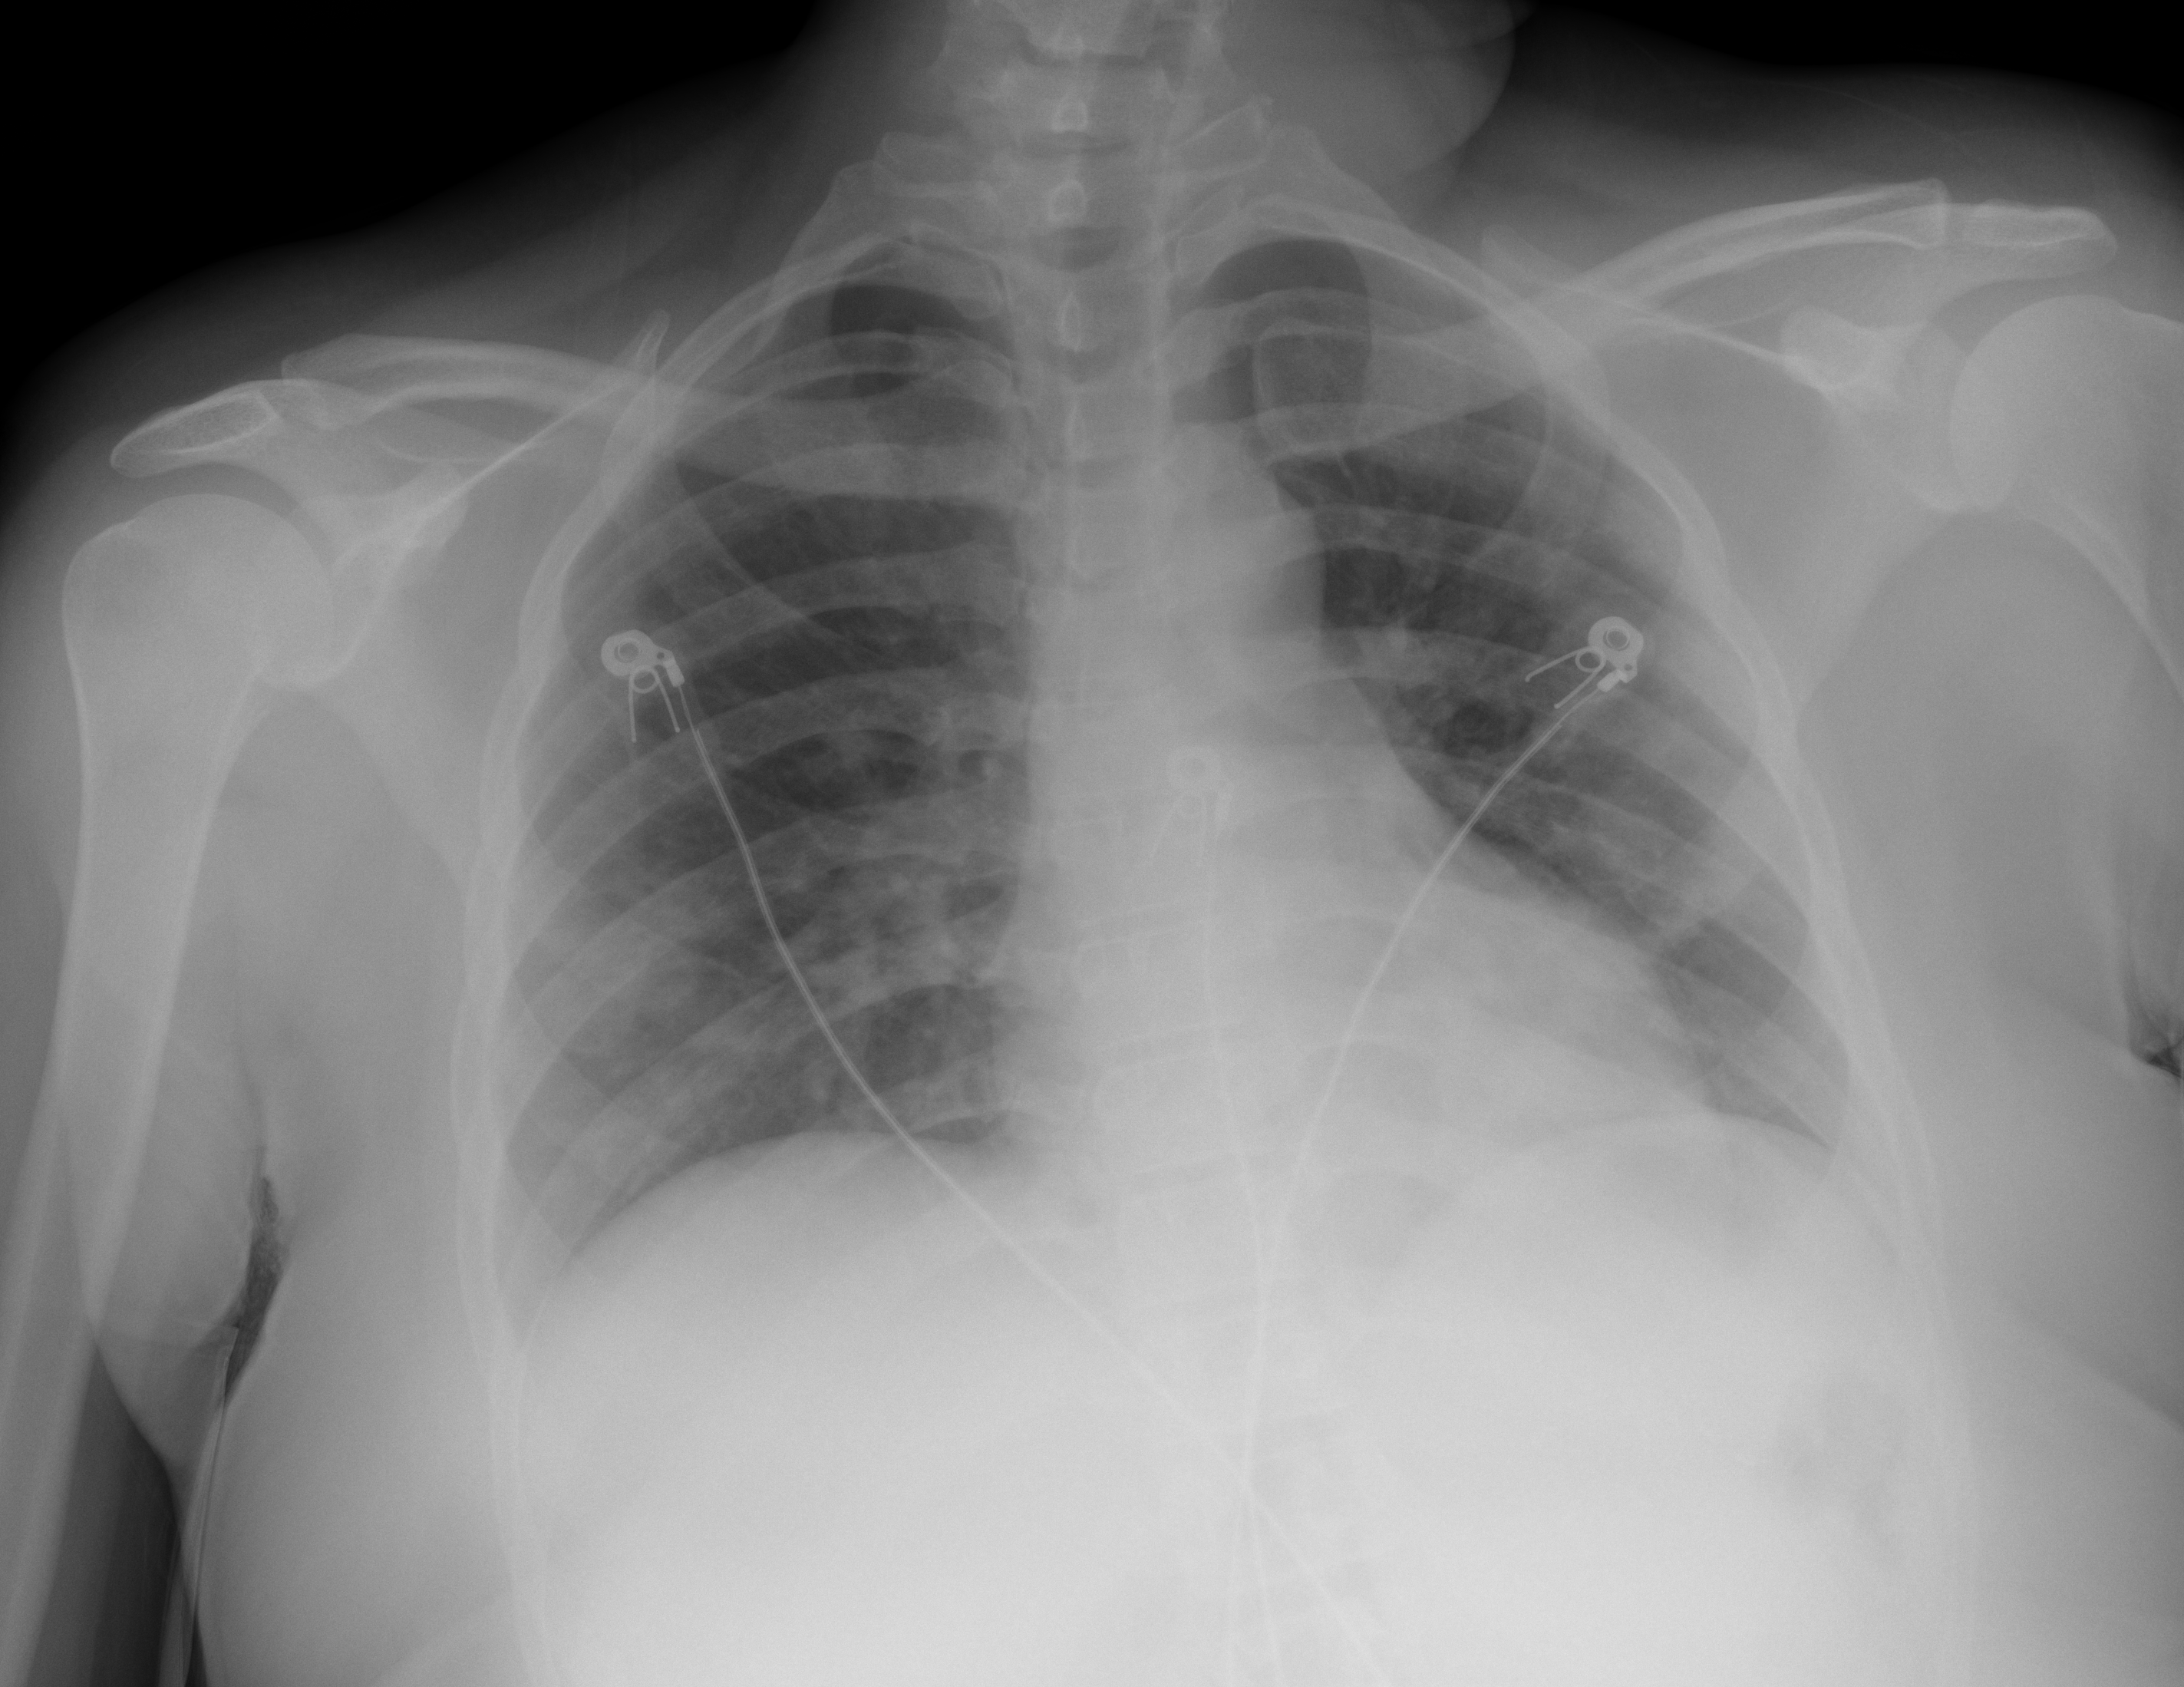
Chest X-ray (portable), AP projection. Female patient, age 29 years; imaged 0 days after the COVID-19 diagnosis.
Radiologist's key findings for this exam: Hazy airspace changes are seen in both lung bases with no evidence of consolidation.